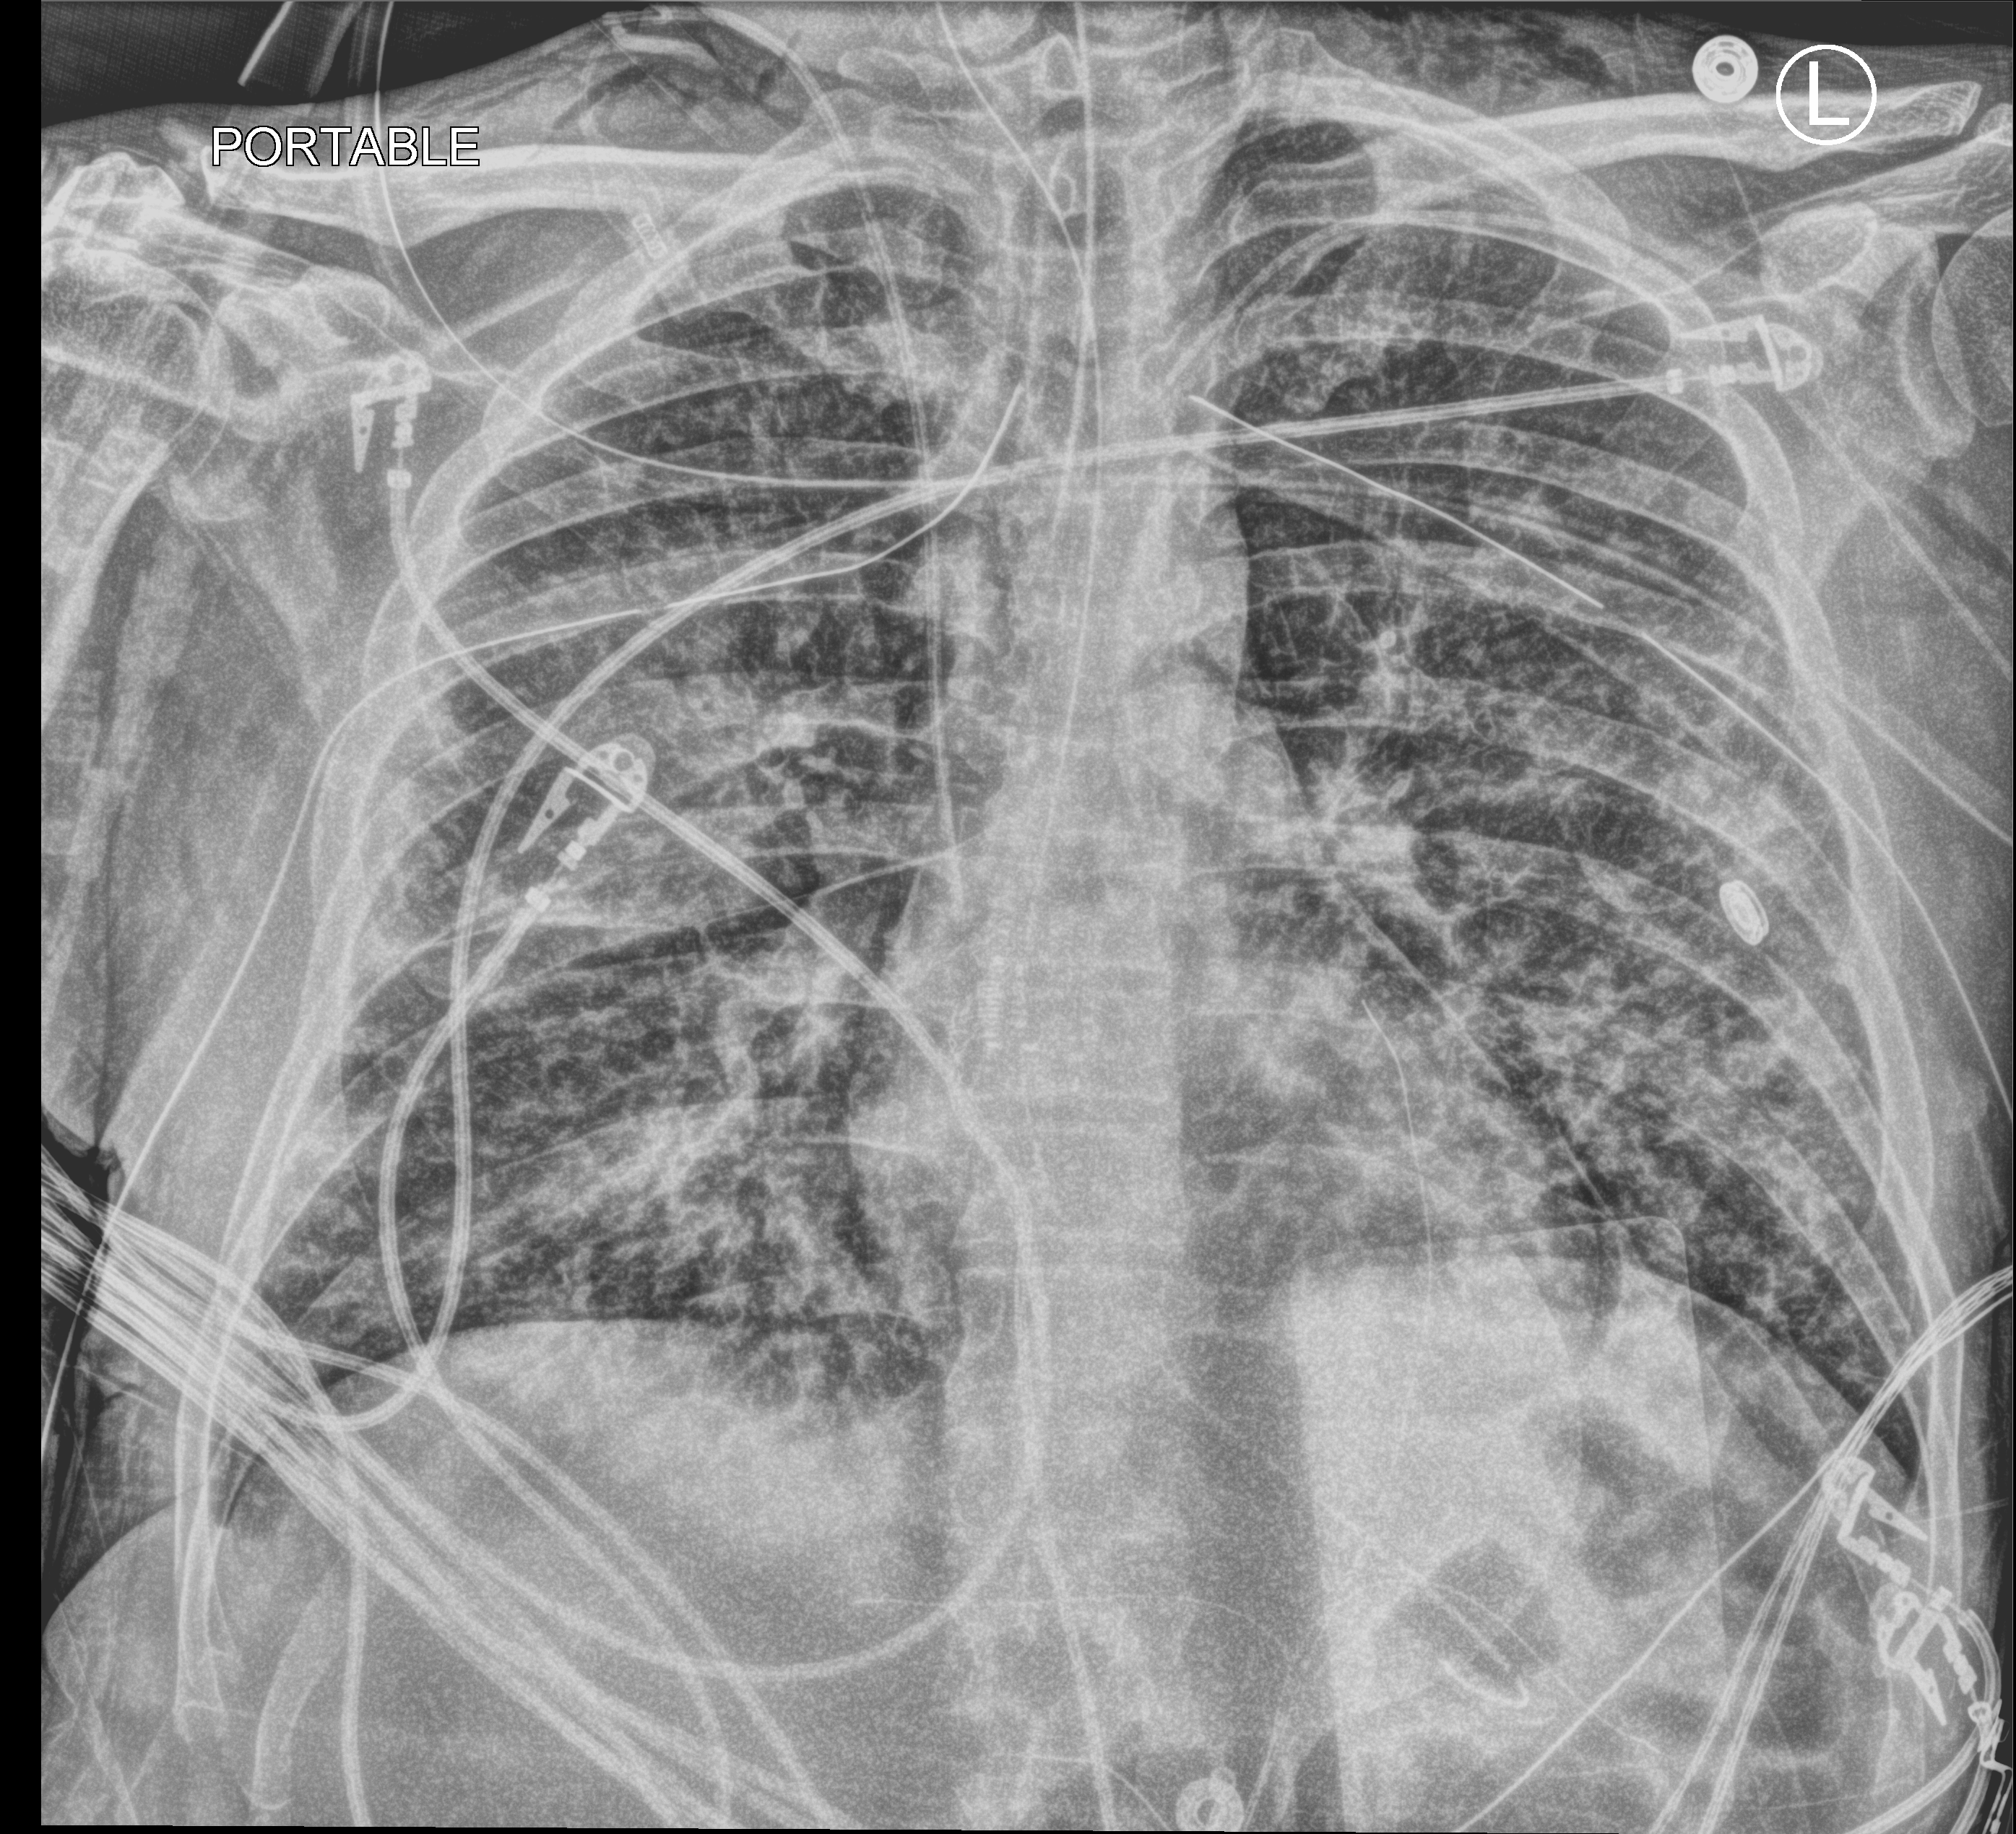
Chest X-ray (portable), anteroposterior (AP) projection. Patient hospitalised with COVID-19; male, aged 18–59 years.
Hospital-stay facts (about this admission, not read from this image; timing relative to this image not recorded):
- admitted to intensive care during this hospital stay: yes